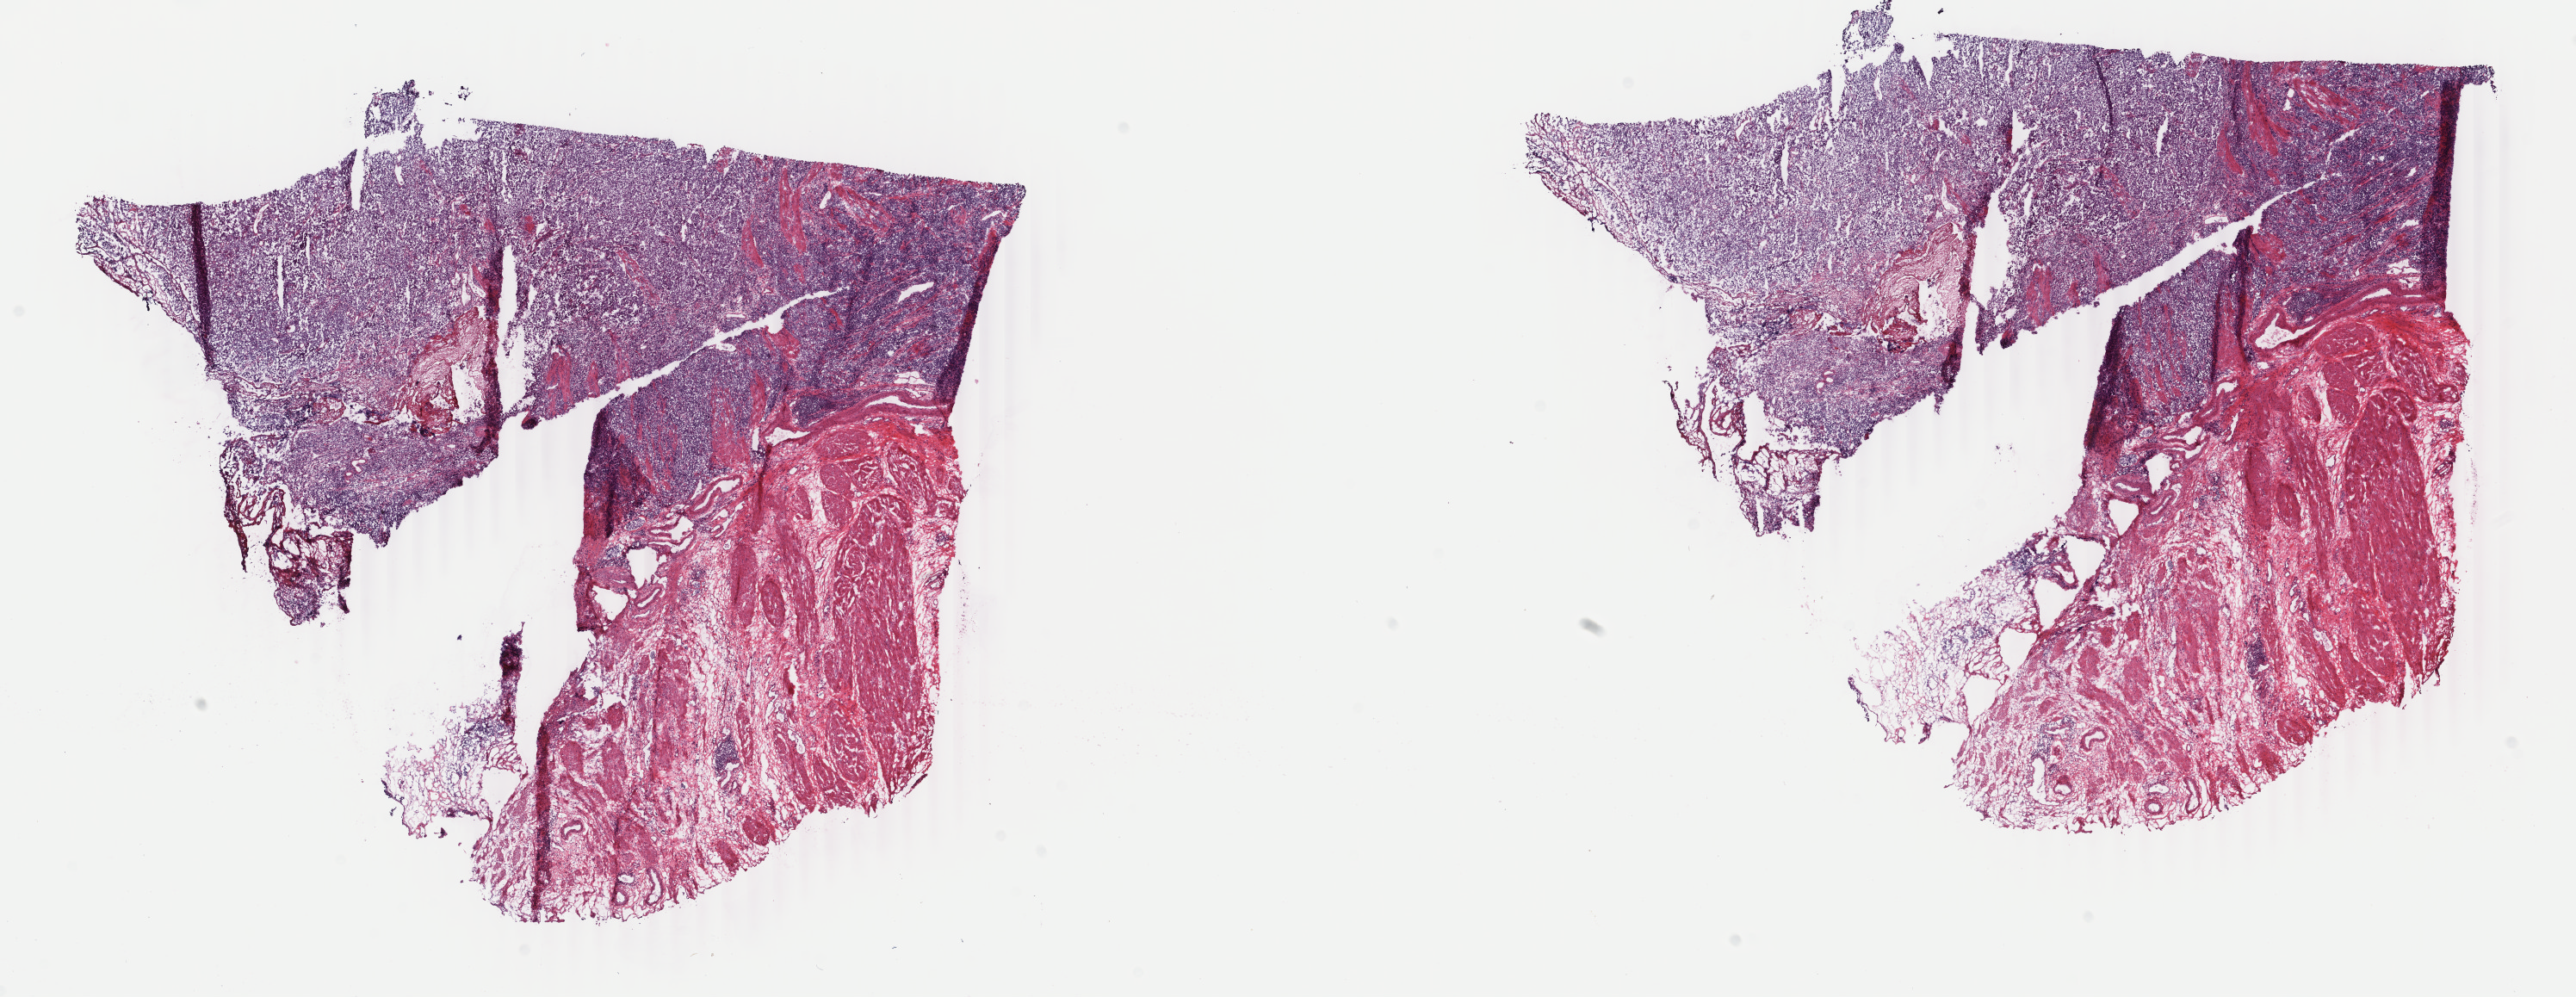
Digitized Hematoxylin and eosin (H&E) stained tissue section (whole slide), whole scanned area (about 23.8 x 9.2 mm, from a 40x scan) shown as a low-resolution overview, frozen section, primary tumour sample from the bladder. Male, age 75 years at initial diagnosis. Histologic grade: high grade. Pathologist review of this section (percent, as recorded): tumour cells 60%, tumour nuclei 60%, normal cells 20%, stromal cells 20%, necrosis 0%. Infiltration values recorded for this section: lymphocyte infiltration 6%, monocyte infiltration 2%, neutrophil infiltration 2%.
- AJCC pathologic stage: II (7th edition)
- histologic diagnosis: Transitional cell carcinoma (anterior wall of bladder)